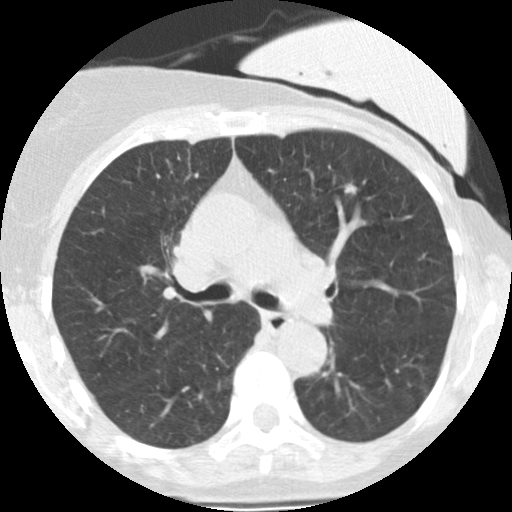
Low-dose screening chest CT, one axial slice. Slice 158 of 251 in the series (ordered by position). Reconstruction kernel STANDARD. Lung window (W 1500 / L -600 HU). 2.5 mm slice thickness. 512 × 512 image matrix, field of view 280 × 280 mm.
Structures marked on this image (expert manual segmentation):
- lesion 1 (tumor, lower lobe of left lung): bounding box <345,183,357,194> (left, top, right, bottom; pixels)